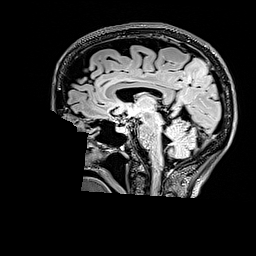
Brain MRI from a brain-tumour surgery series, one sagittal slice. Slice 94 of 176 in the series (ordered by position). T2 FLAIR. 1 mm slice thickness. 256 × 256 image matrix, field of view 256 × 256 mm. From the clinical record (not read from this slice): histopathology: Astrocytoma; WHO grade: 3; IDH mutation: yes.
Annotated regions visible in this slice (expert manual segmentation):
- tumour: box from (x=185, y=57) to (x=206, y=82) px
- tumour: (x=185, y=58)–(x=207, y=80)